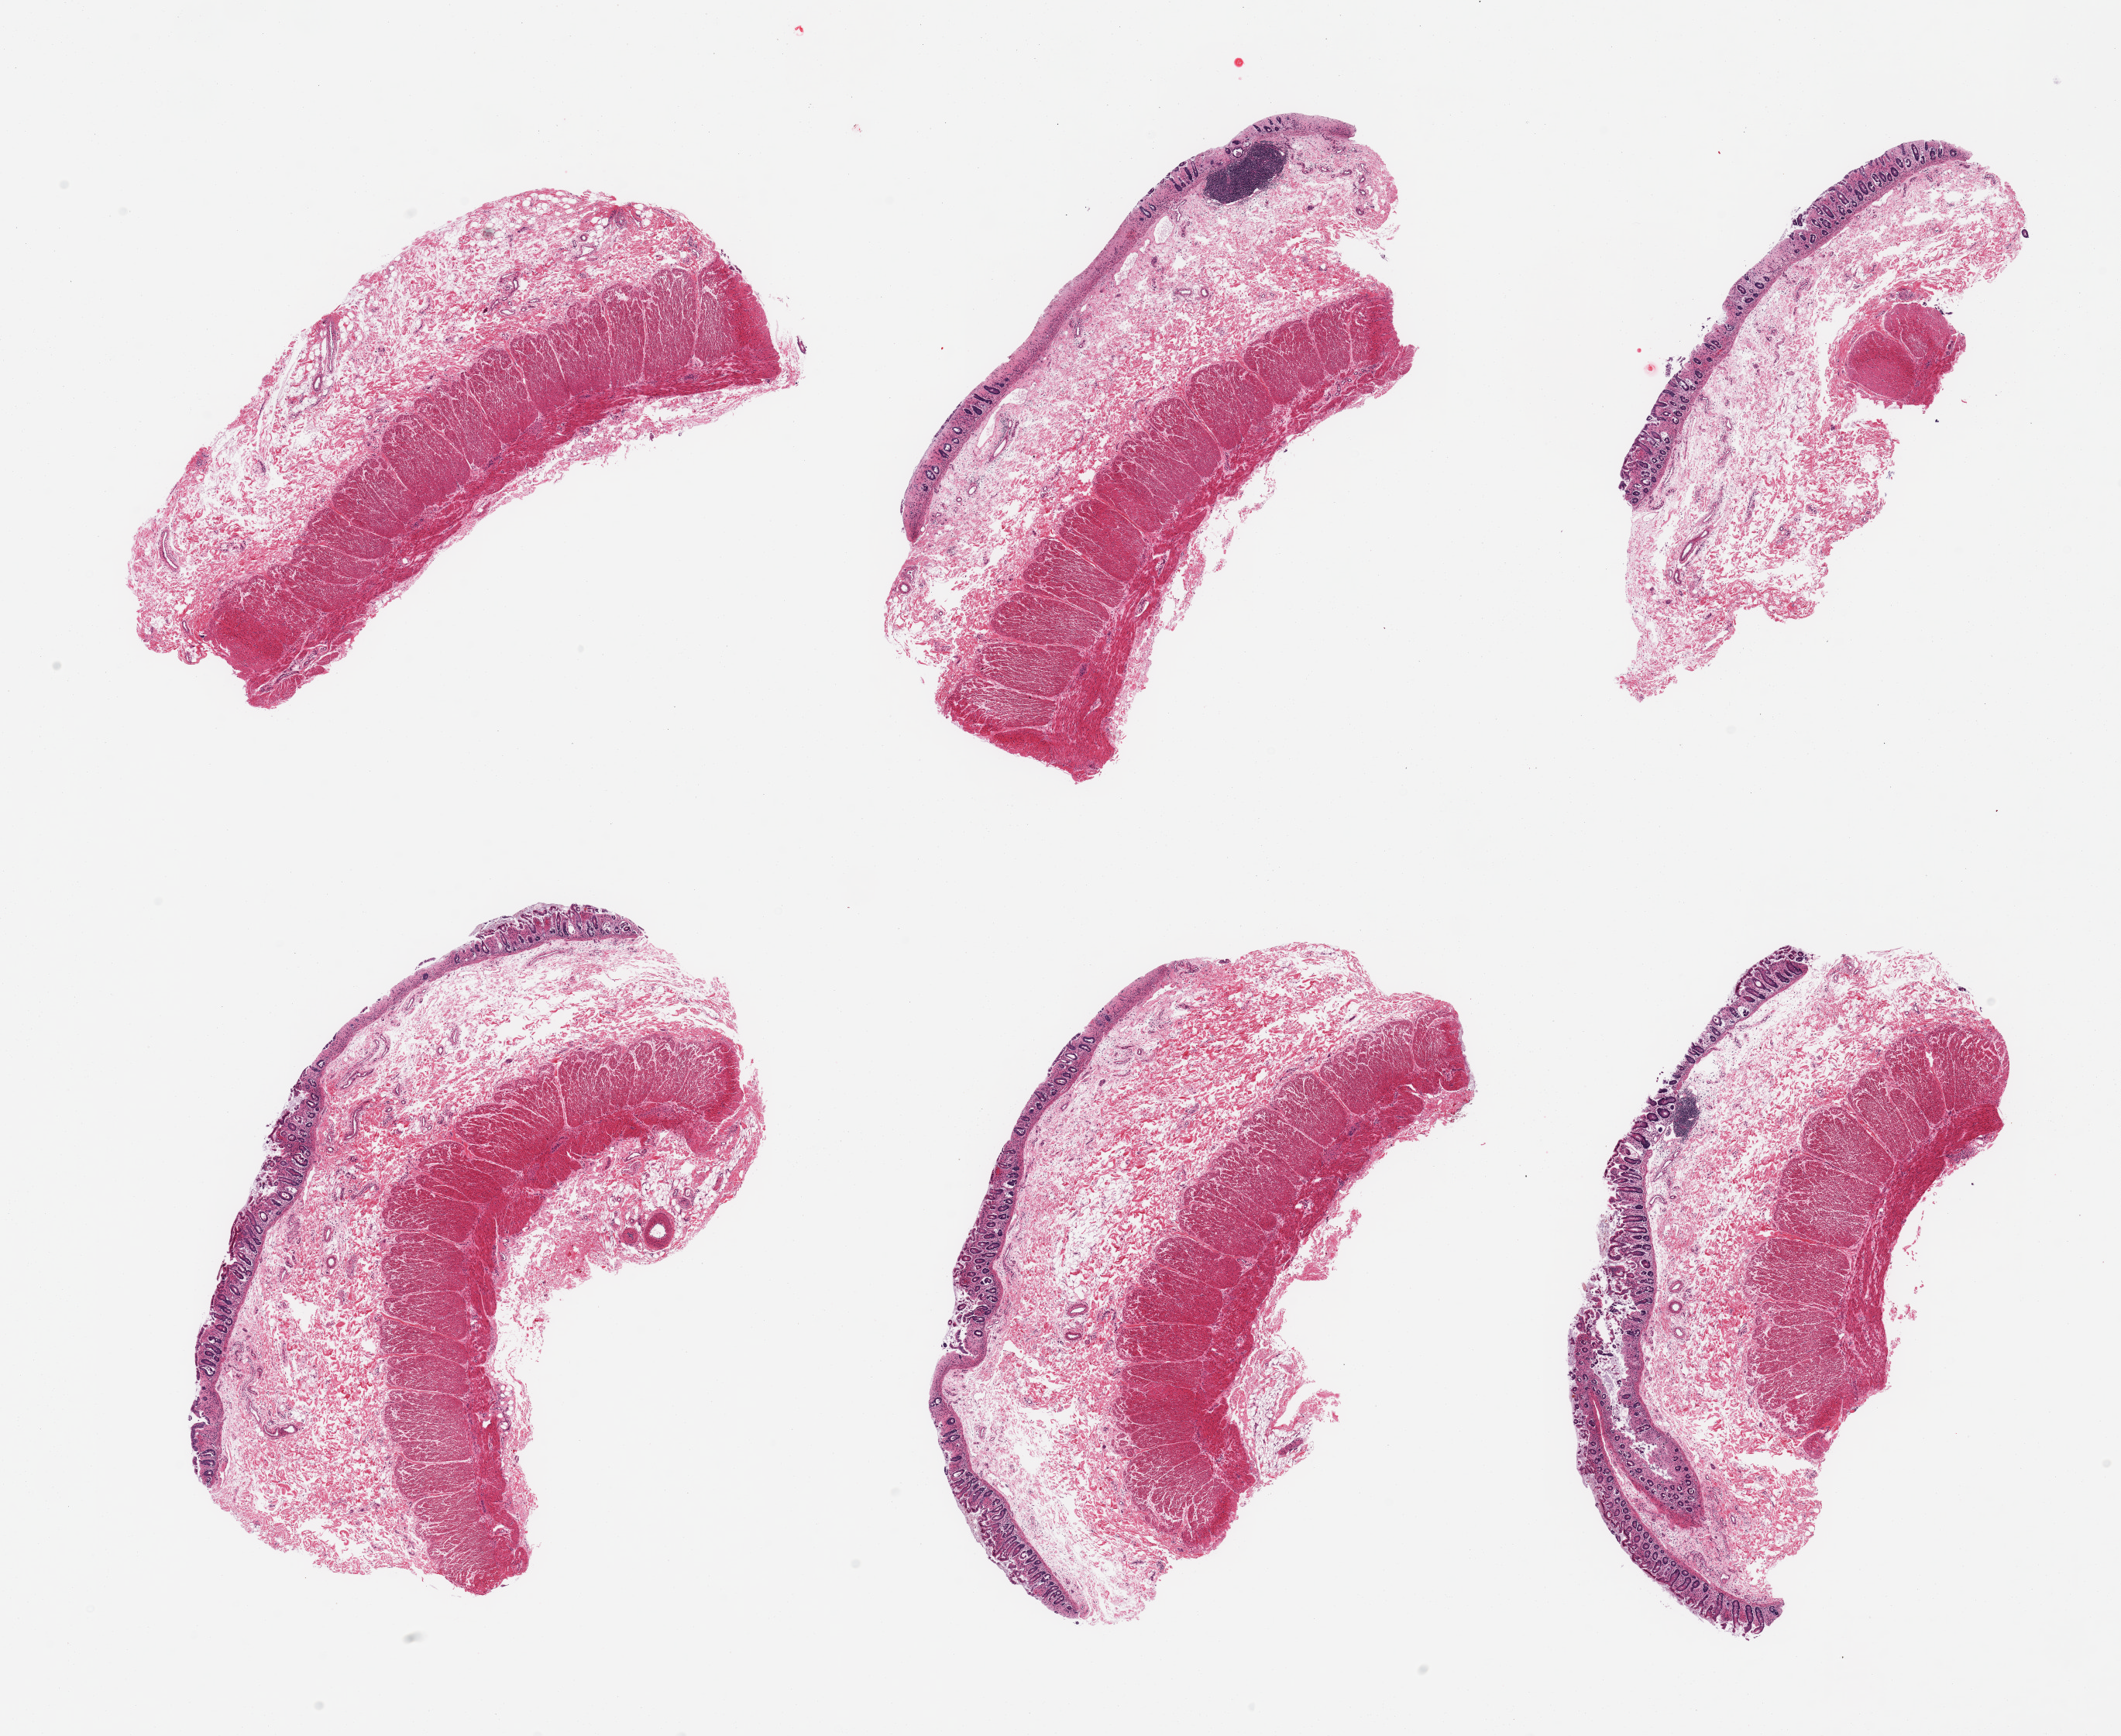
Whole-slide image, hematoxylin and eosin (H&E) stain, brightfield — a low-resolution overview of the entire scanned area, about 21.7 x 17.7 mm; PAXgene-fixed, paraffin-embedded tissue; section of transverse colon (target tissue); donor tissue sample. Donor: female.
Review note (as recorded): 6 pieces; mucosa moderate autolysis, muscularis slight autolysis; 1 has no mucosa.